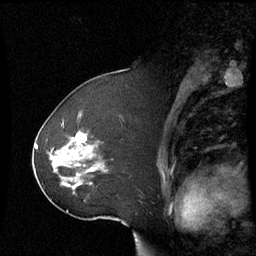
Breast MRI (dynamic contrast-enhanced), one sagittal slice; slice 39 of 60 in the series (ordered by position); dynamic contrast-enhanced series, image 2 of 3 at this slice position (ordered by acquisition); 1.5 T; TE 4.2 ms, TR 8.9 ms; 2.4 mm slice thickness; 256 × 256 image matrix, field of view 230 × 230 mm. Patient: female, 51 years. From the clinical record (not read from this slice): setting: breast cancer imaged before/during neoadjuvant chemotherapy; receptor status: HR-positive, HER2-negative.
Outlined on this slice (semi-automatic segmentation, software-assisted and operator-edited):
- analysis volume of interest (the breast-tissue region the enhancement analysis was run in; not a lesion): bounding box (x1, y1, x2, y2) in pixels: (42, 122, 105, 199)
- tumour enhancement mask (voxels above the 70 % enhancement threshold inside the analysis volume of interest): (76, 133, 93, 171)